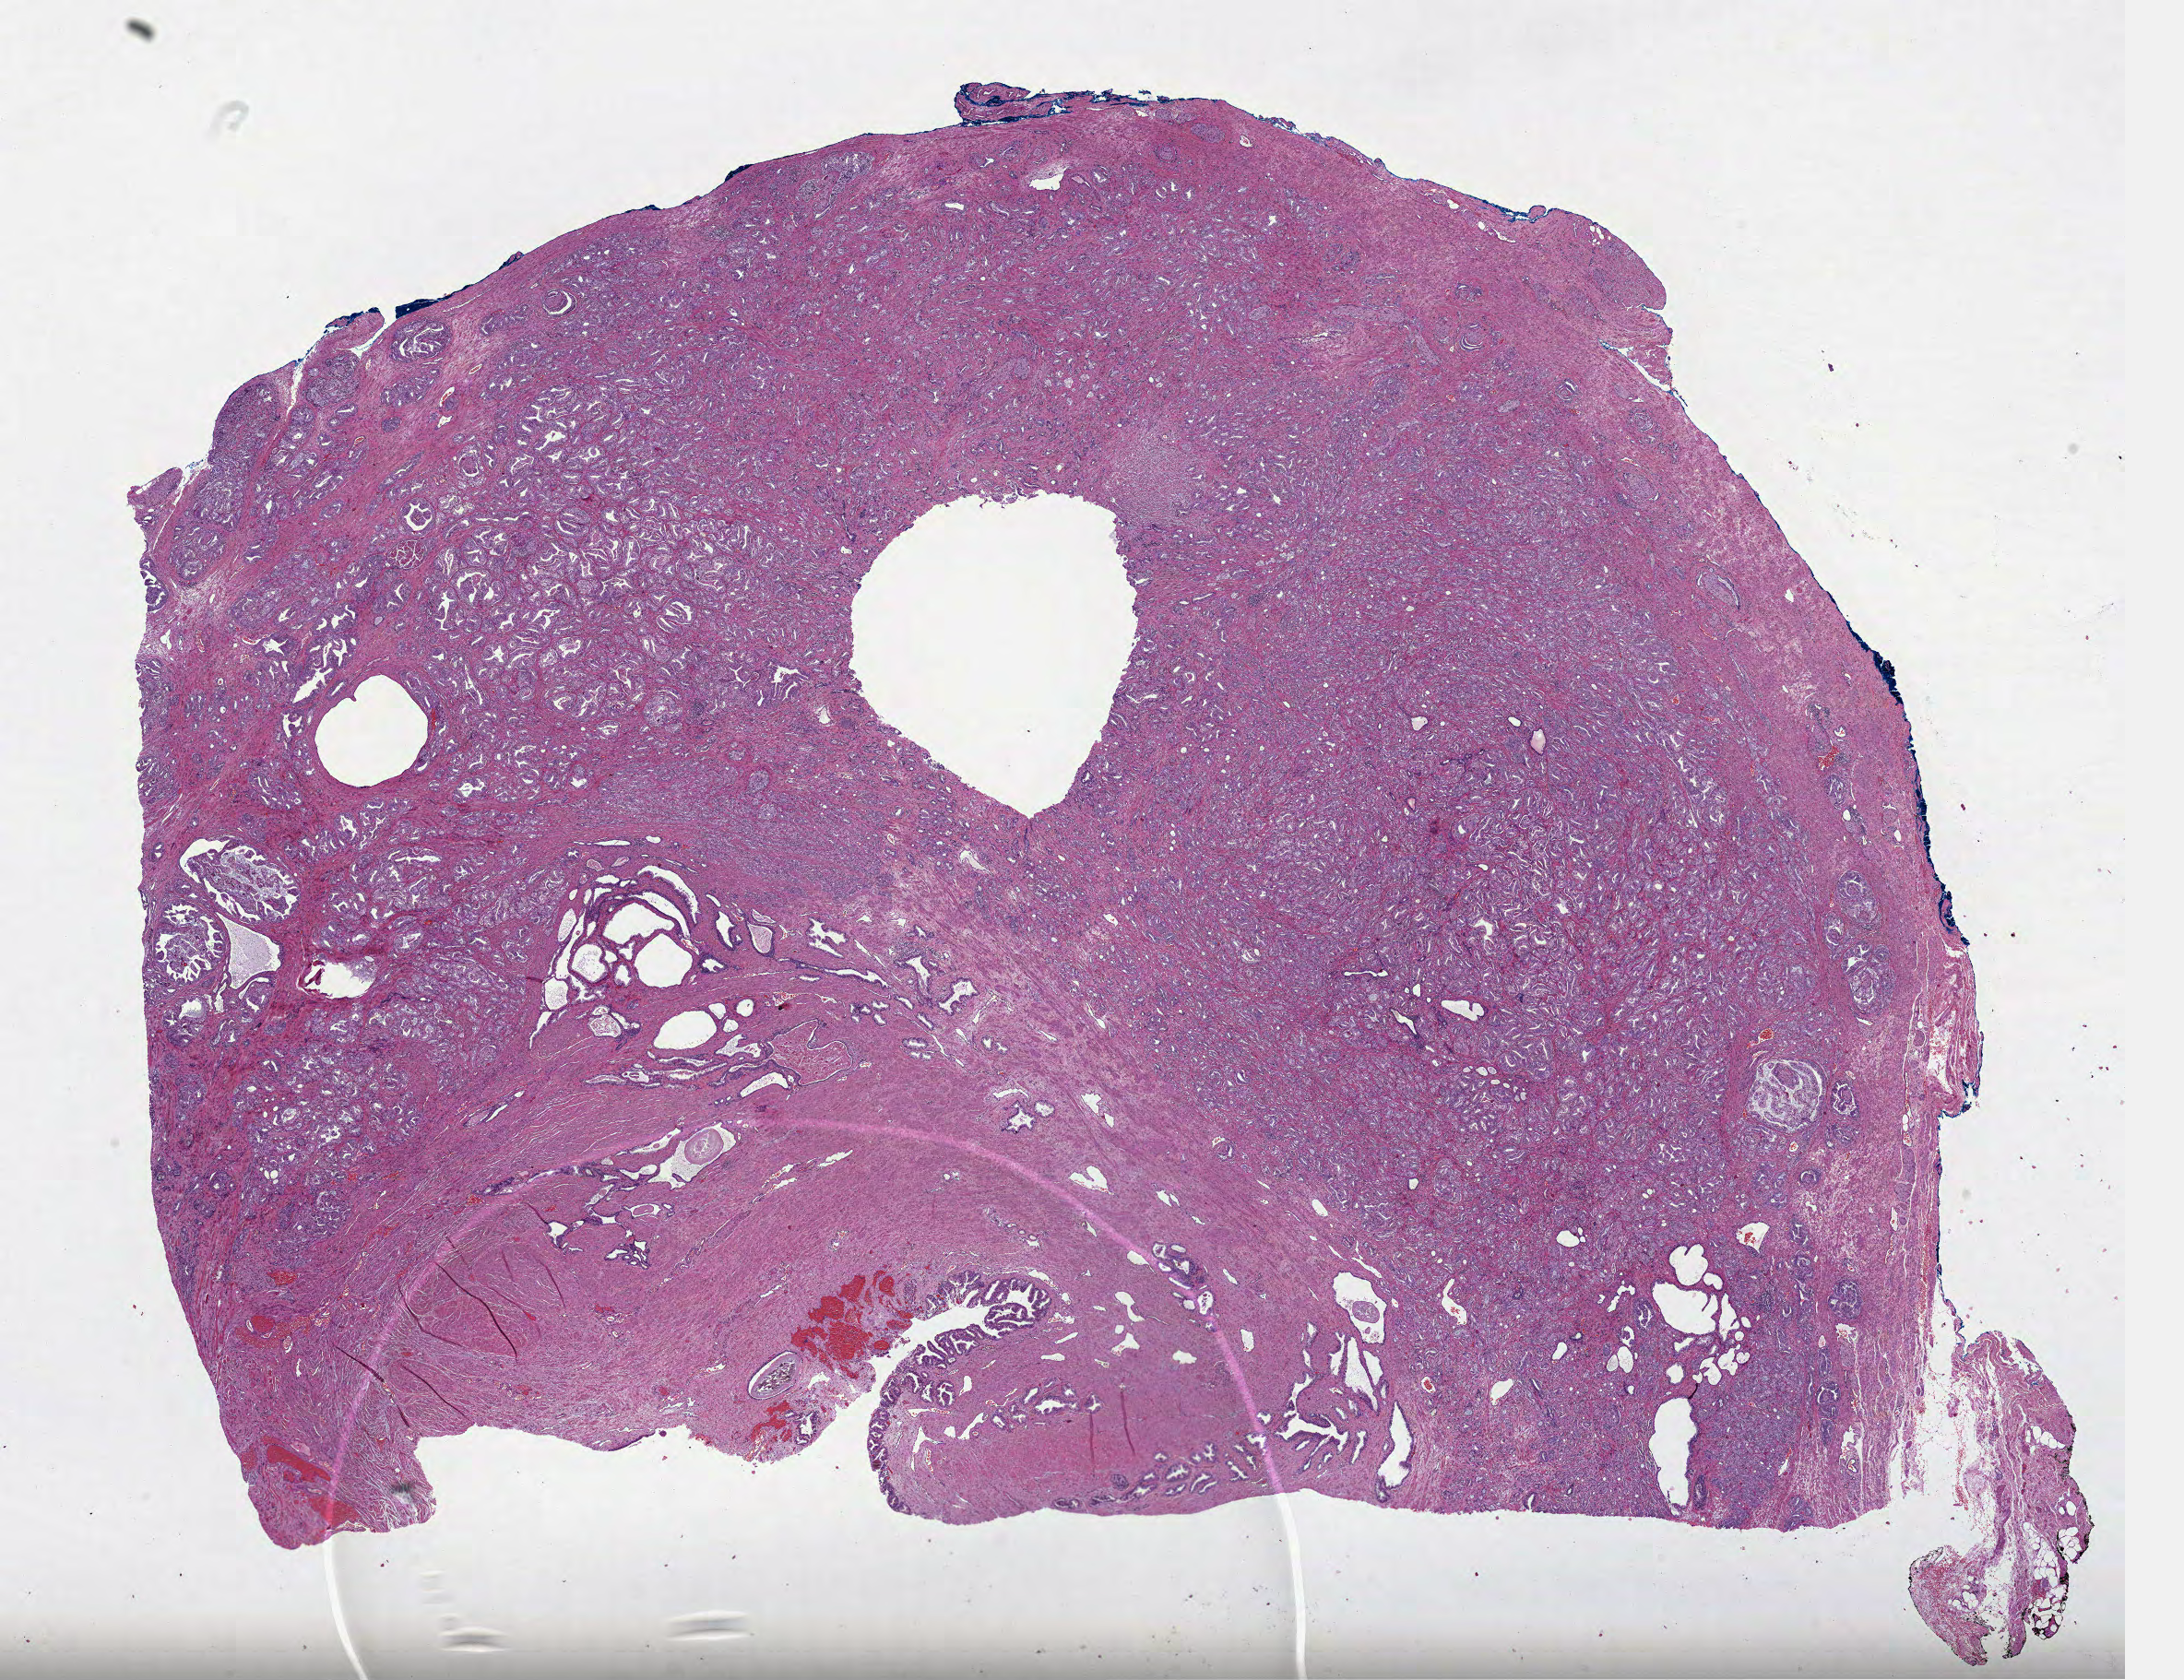
H&E whole-slide image, low-resolution overview of the scanned area, about 19.1 x 14.7 mm (slide scanned at 40x). Formalin-fixed paraffin-embedded (FFPE) diagnostic section. Prostate, primary tumour sample. Male patient; age at initial diagnosis 67 years. Gleason score: 7 (4+3).
- histologic diagnosis: Adenocarcinoma, NOS (prostate gland)
- laterality: bilateral
- lymph nodes positive (case pathology): 0 of 1 examined